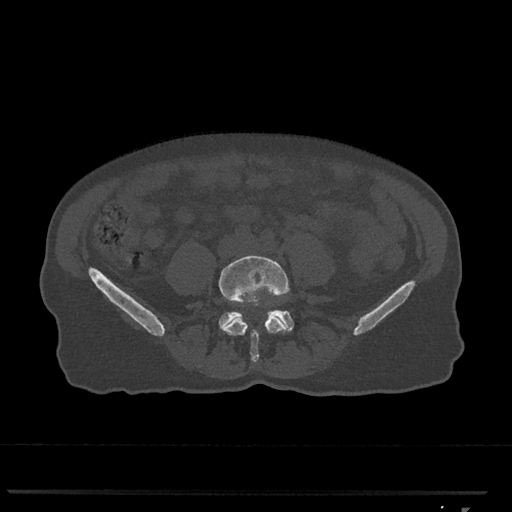
CT including the spine, one axial slice; position 185 of 793 along the scan axis; 120 kVp; bone window (W 1800 / L 400 HU); 0.5 mm slice thickness; 512 × 512 image matrix, field of view 380 × 380 mm. Female patient, age 62 years. Case-level facts recorded for this patient, not image findings: primary cancer: renal.
Annotated regions visible in this slice (semi-automatically segmented with operator editing):
- L4 vertebra: bounding box (x1, y1, x2, y2) in pixels: (219, 255, 291, 362)
- L5 vertebra: (219, 310, 294, 330)